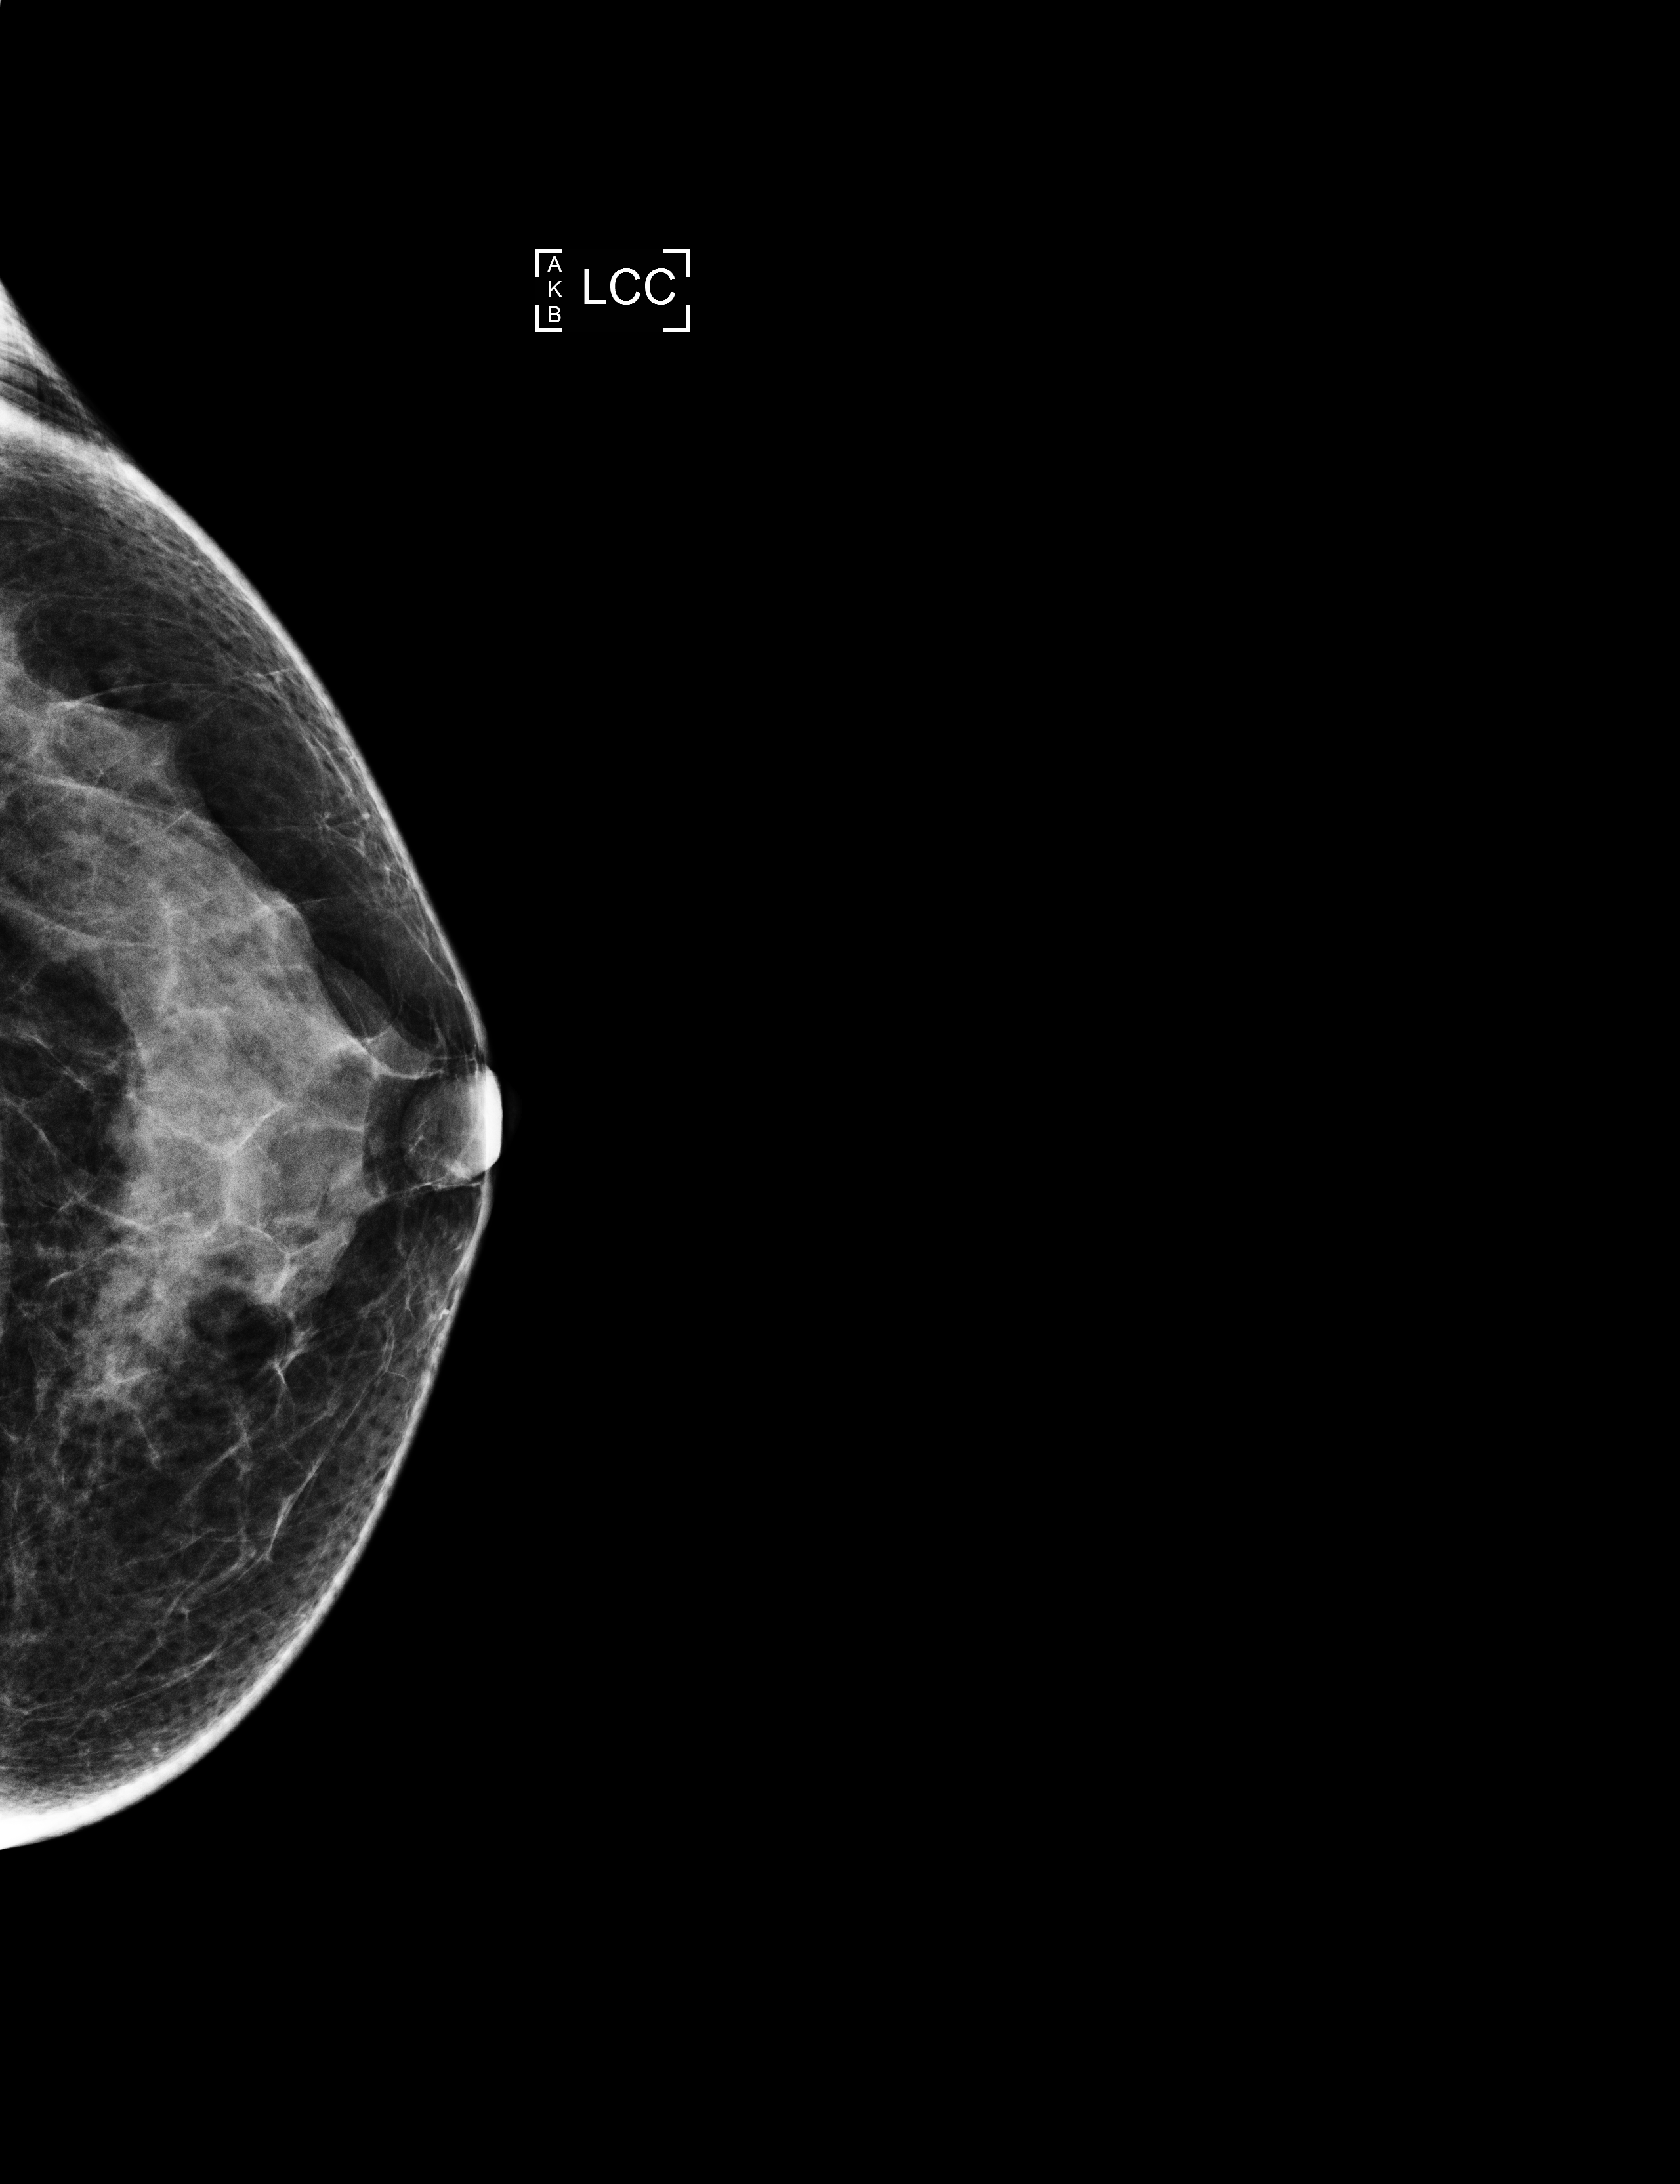
Screening examination, compressed breast thickness 39 mm. Female patient, age 57 years.
Image type: full-field digital mammogram. Breast: left. Projection: craniocaudal (CC) view.